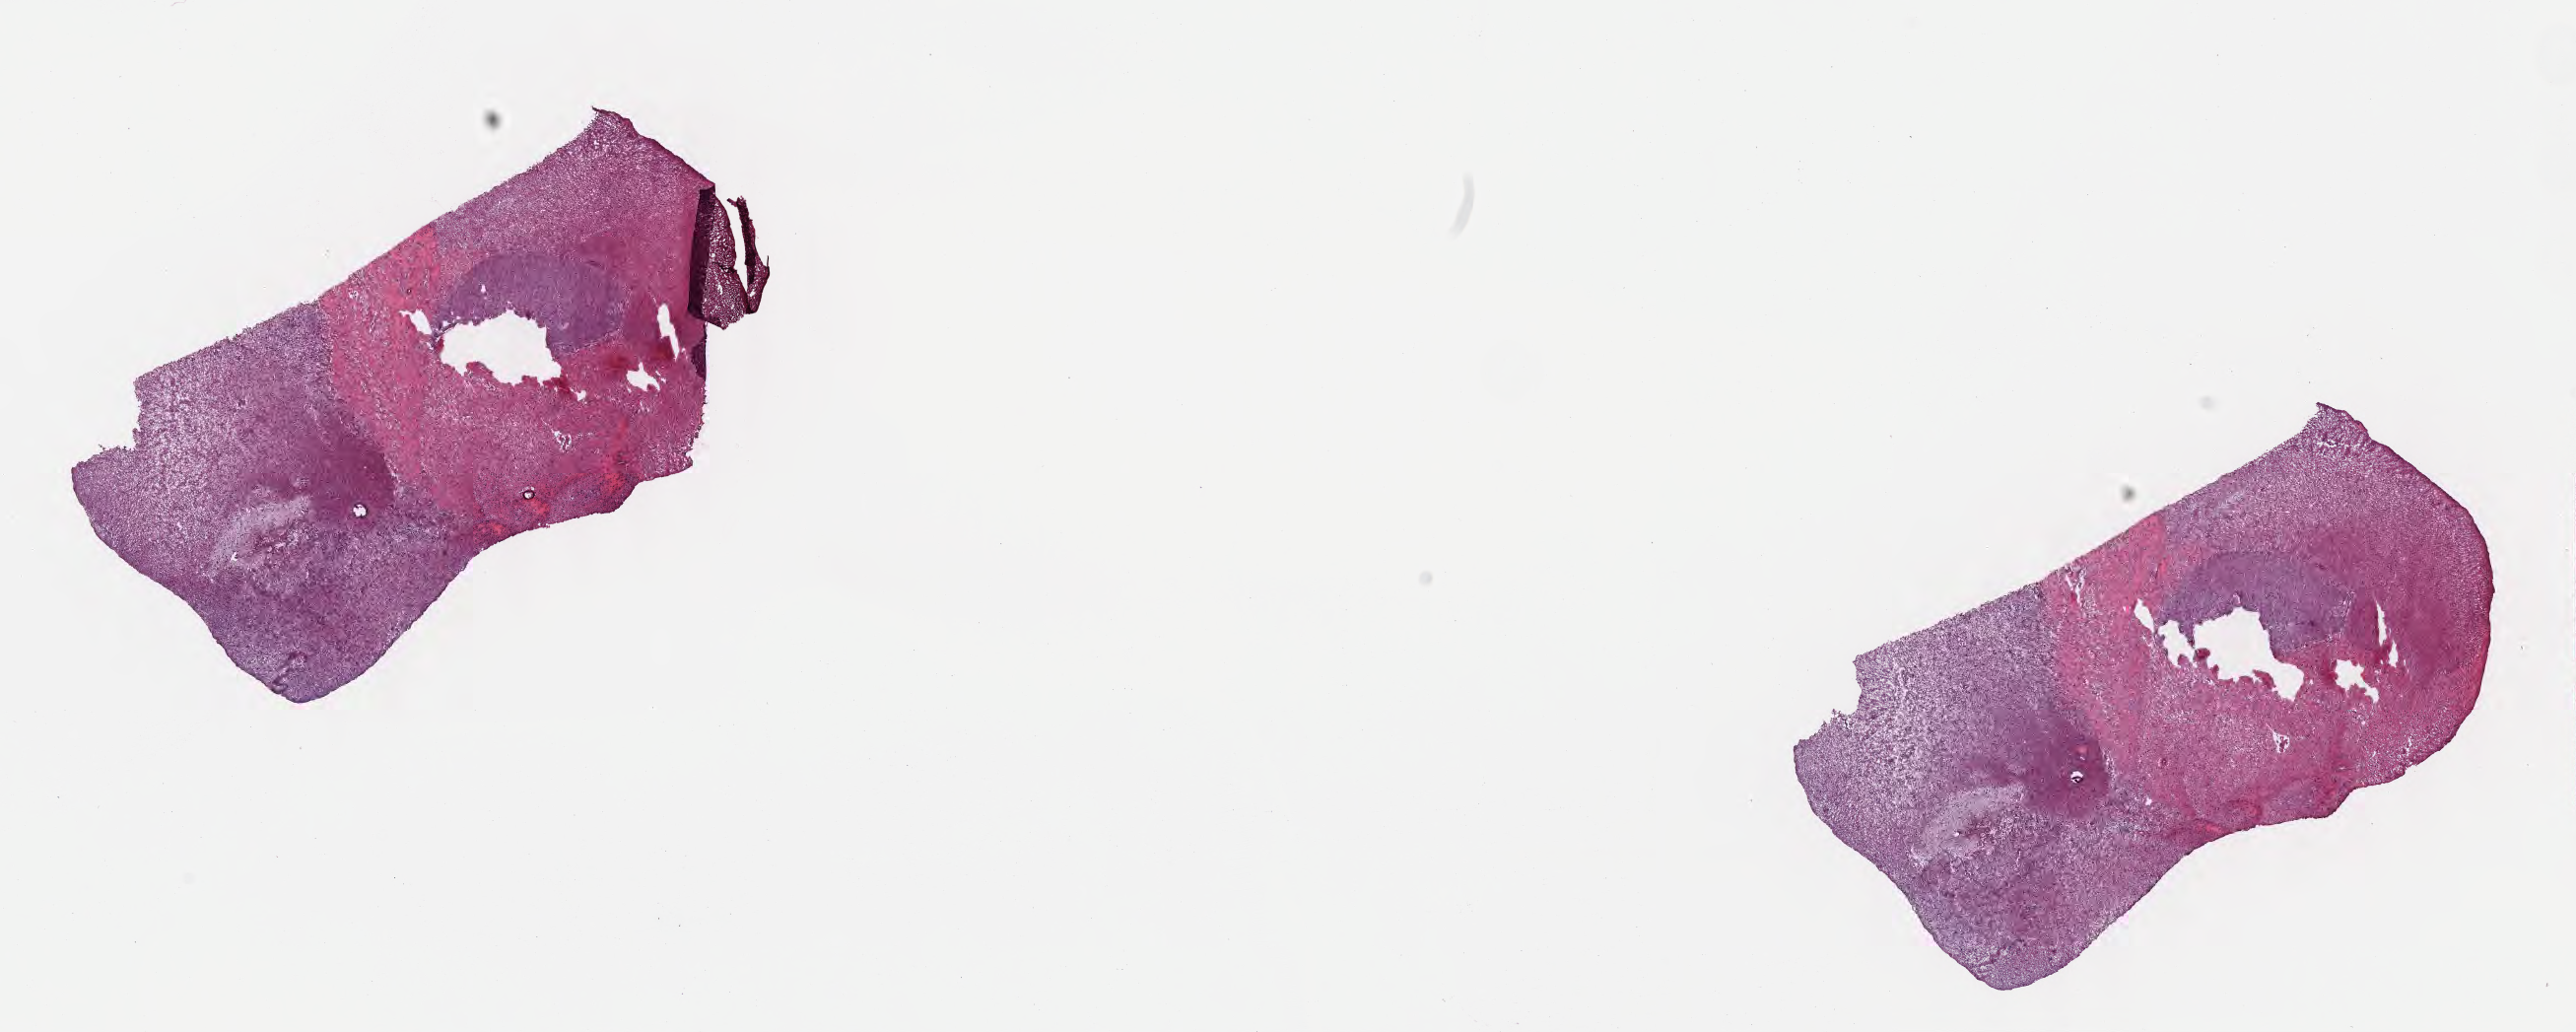
Digitized hematoxylin and eosin (H&E)-stained section — low-resolution overview of the scanned area, about 21.1 x 8.5 mm; cryosection; specimen: recurrent tumor; site: brain. Male, age 52 years at initial diagnosis. Slide review estimates, as recorded: tumor cells 46%, tumor nuclei 74%, stromal cells 38%, necrosis 0%, normal cells 16%. Inflammatory infiltration, as recorded: lymphocyte infiltration 1%, monocyte infiltration 0%, neutrophil infiltration 0%.
Patient diagnosis: Glioblastoma, NOS. Section: top of the tissue portion.